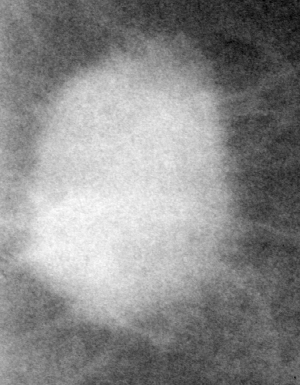
Crop from a digitized film mammogram around one marked abnormality; left breast; CC view.
Mass, shape oval, margins spiculated; BI-RADS assessment category 4; subtlety rating 5 on a 1 (subtle) to 5 (obvious) scale; pathology result (as recorded, not read from the image): malignant.